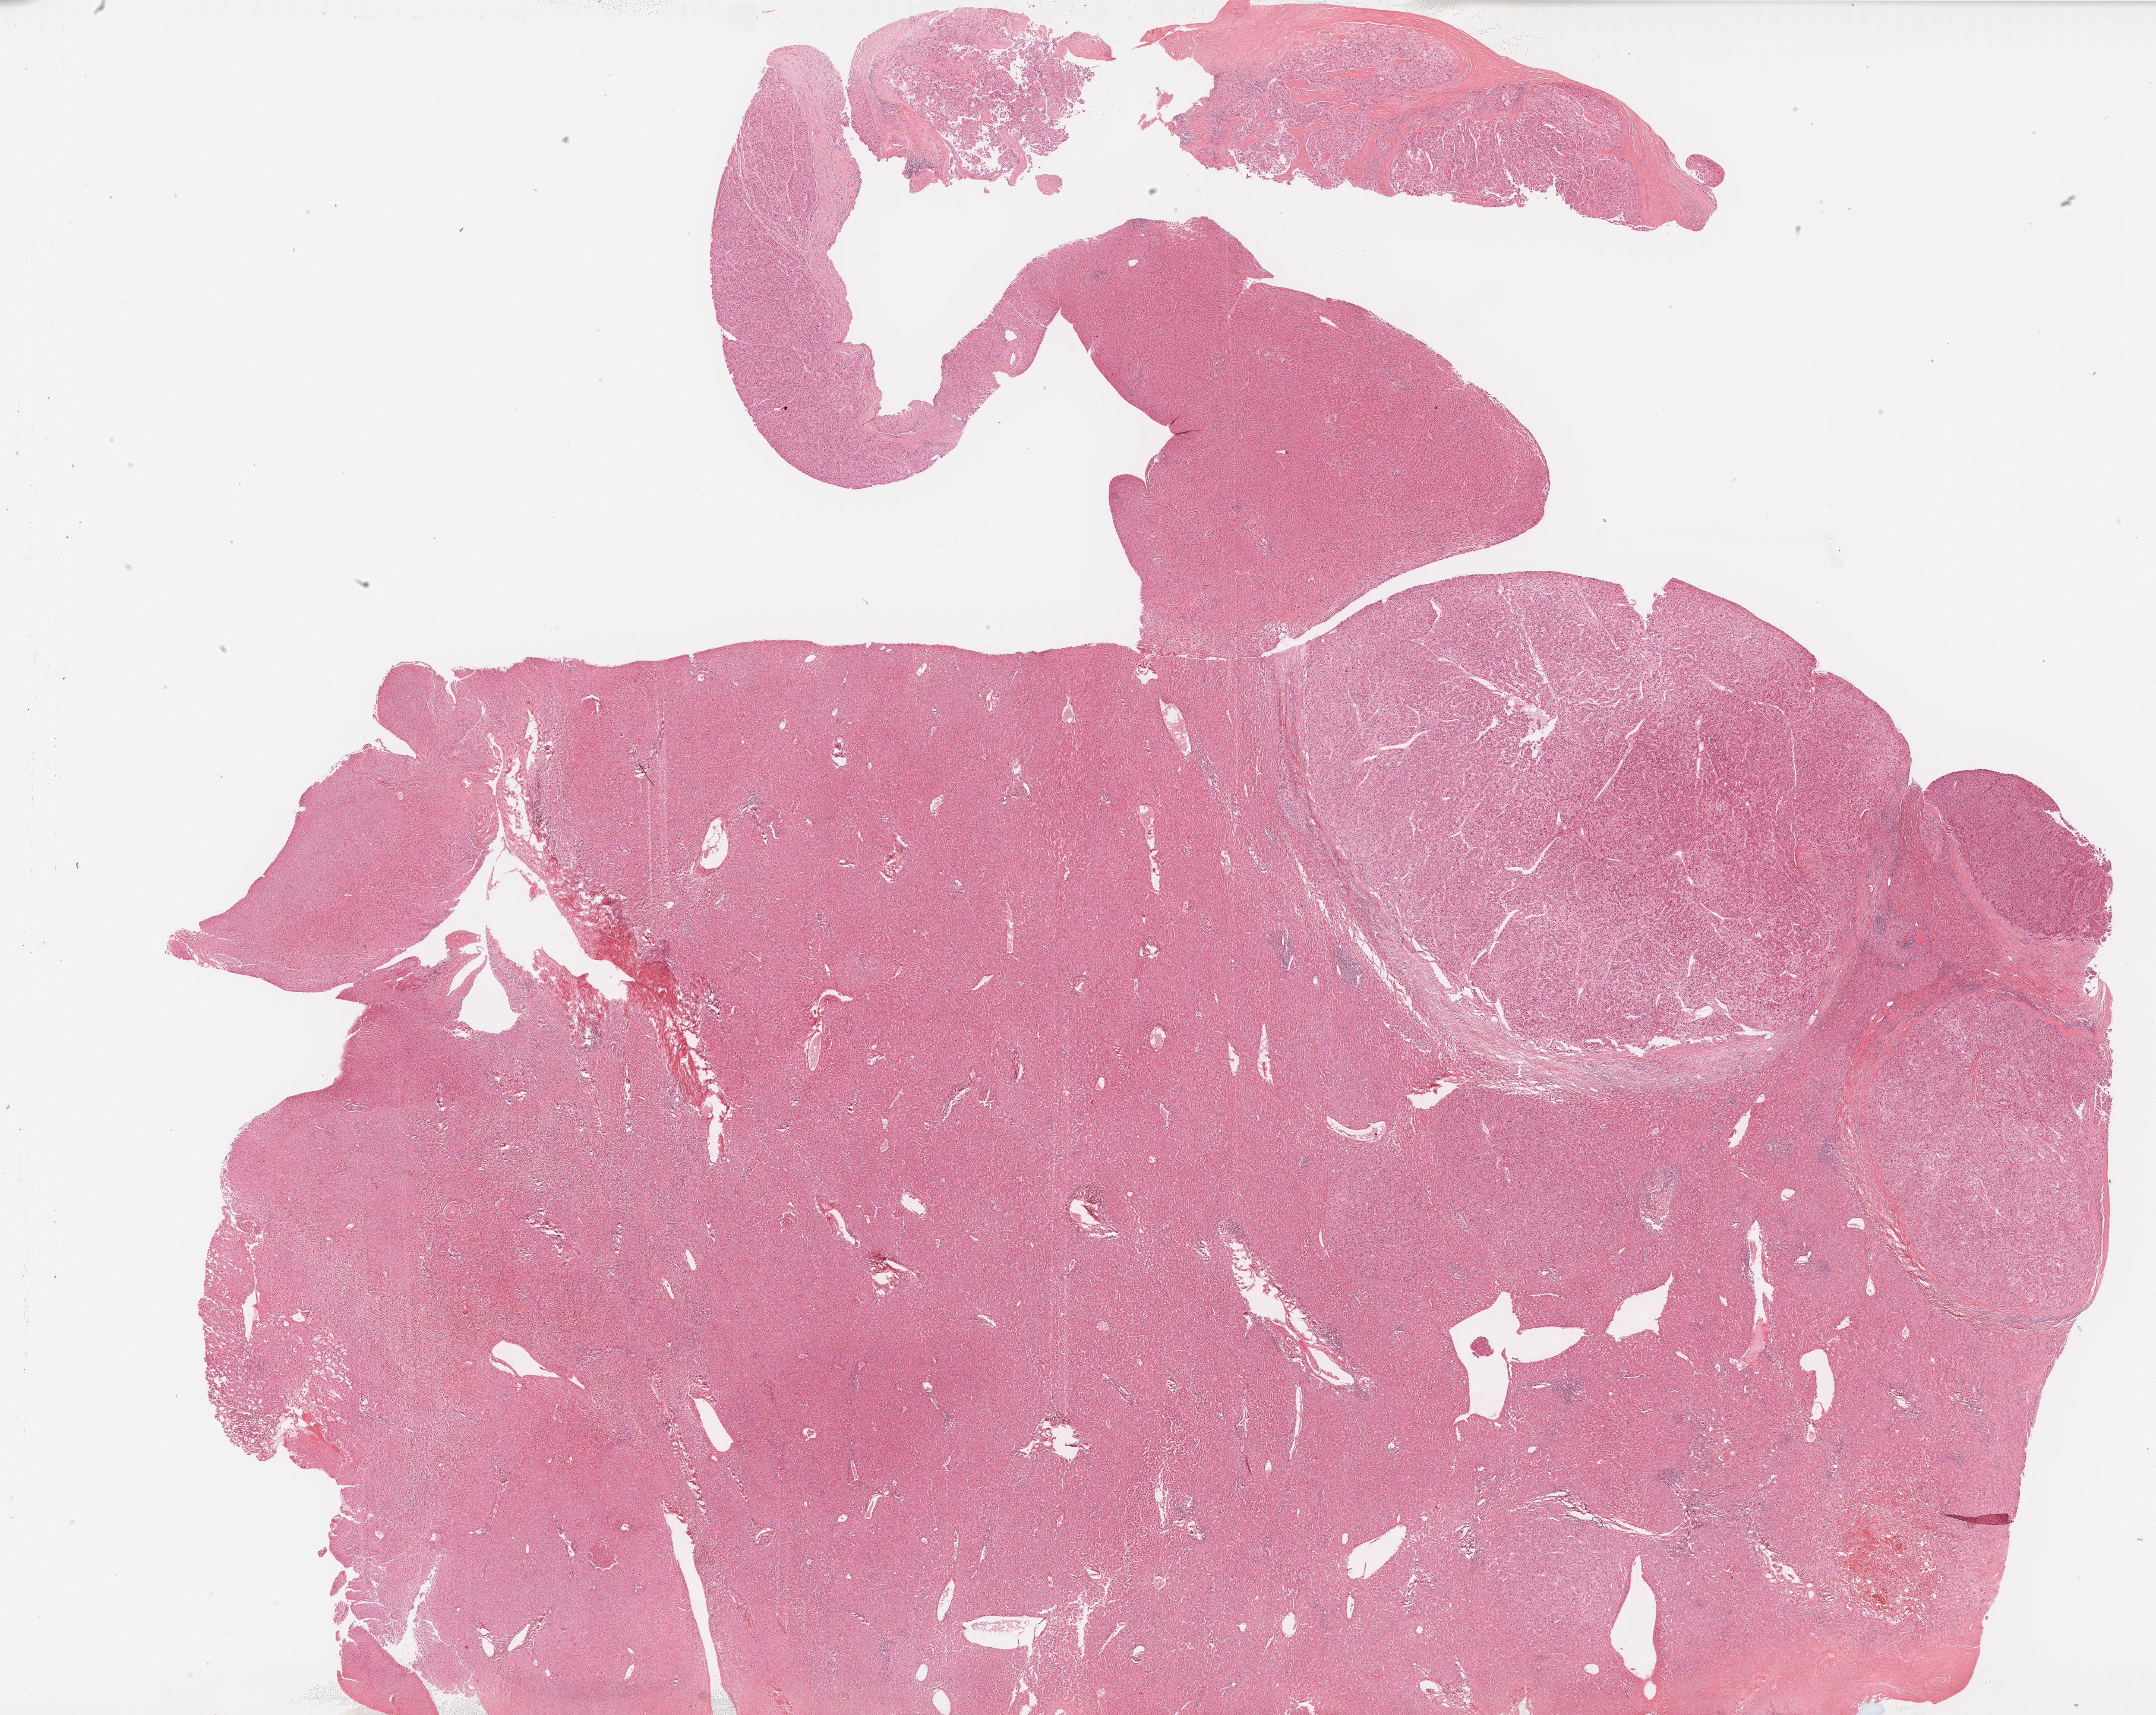
Hematoxylin and eosin (H&E) stained whole-slide image, a low-resolution overview of the entire scanned area, about 29.4 x 23.4 mm. Formalin-fixed paraffin-embedded (FFPE) diagnostic section. Liver, primary tumour sample. Male, age 53 years at initial diagnosis. Histologic grade: G2 (moderately differentiated).
- AJCC pathologic stage: IIIA
- histologic diagnosis: Hepatocellular carcinoma, NOS